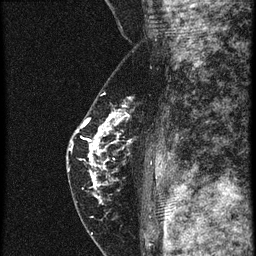
Breast MRI (dynamic contrast-enhanced), one sagittal slice; 4 images stored at this slice position (order not interpretable as contrast timing); 1.5 T; TE 4.2 ms, TR 20.4 ms; 1.5 mm slice thickness; 256 × 256 image matrix, field of view 180 × 180 mm. Patient: female, 46 years. Case-level facts recorded for this patient, not image findings: setting: breast cancer imaged before/during neoadjuvant chemotherapy; receptor status: triple-negative.
Annotated regions visible in this slice (semi-automatic segmentation, software-assisted and operator-edited):
- analysis volume of interest (the breast-tissue region the enhancement analysis was run in; not a lesion): bounding box <67,82,154,201> (left, top, right, bottom; pixels)
- tumour enhancement mask (voxels above the 90 % enhancement threshold inside the analysis volume of interest): <70,110,124,187>